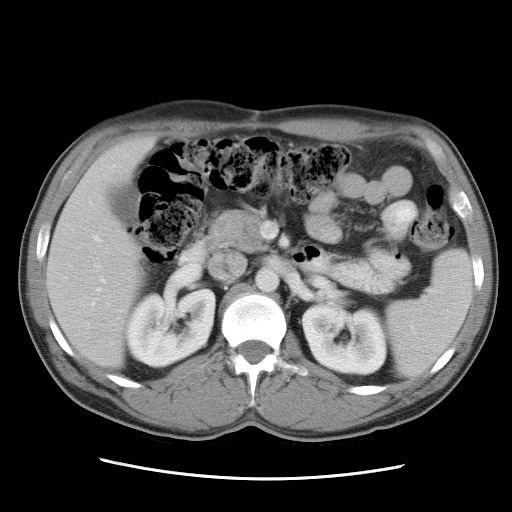
Contrast-enhanced abdominal CT, one axial slice. Reconstruction kernel STANDARD. Intravenous contrast given. Soft-tissue window (W 400 / L 40 HU). 7.5 mm slice thickness. 512 × 512 image matrix. Male patient, age 40 years. Case-level facts recorded for this patient, not image findings: diagnosis: colorectal cancer liver metastases, imaged before liver resection; multiple liver metastases: yes.
Annotated regions visible in this slice (expert manual segmentation):
- liver: box from (x=47, y=138) to (x=155, y=367) px
- planned liver remnant (the part of the liver to remain after resection): (x=47, y=138)–(x=155, y=367)
- portal vein (with intrahepatic branches): (x=92, y=236)–(x=105, y=306)